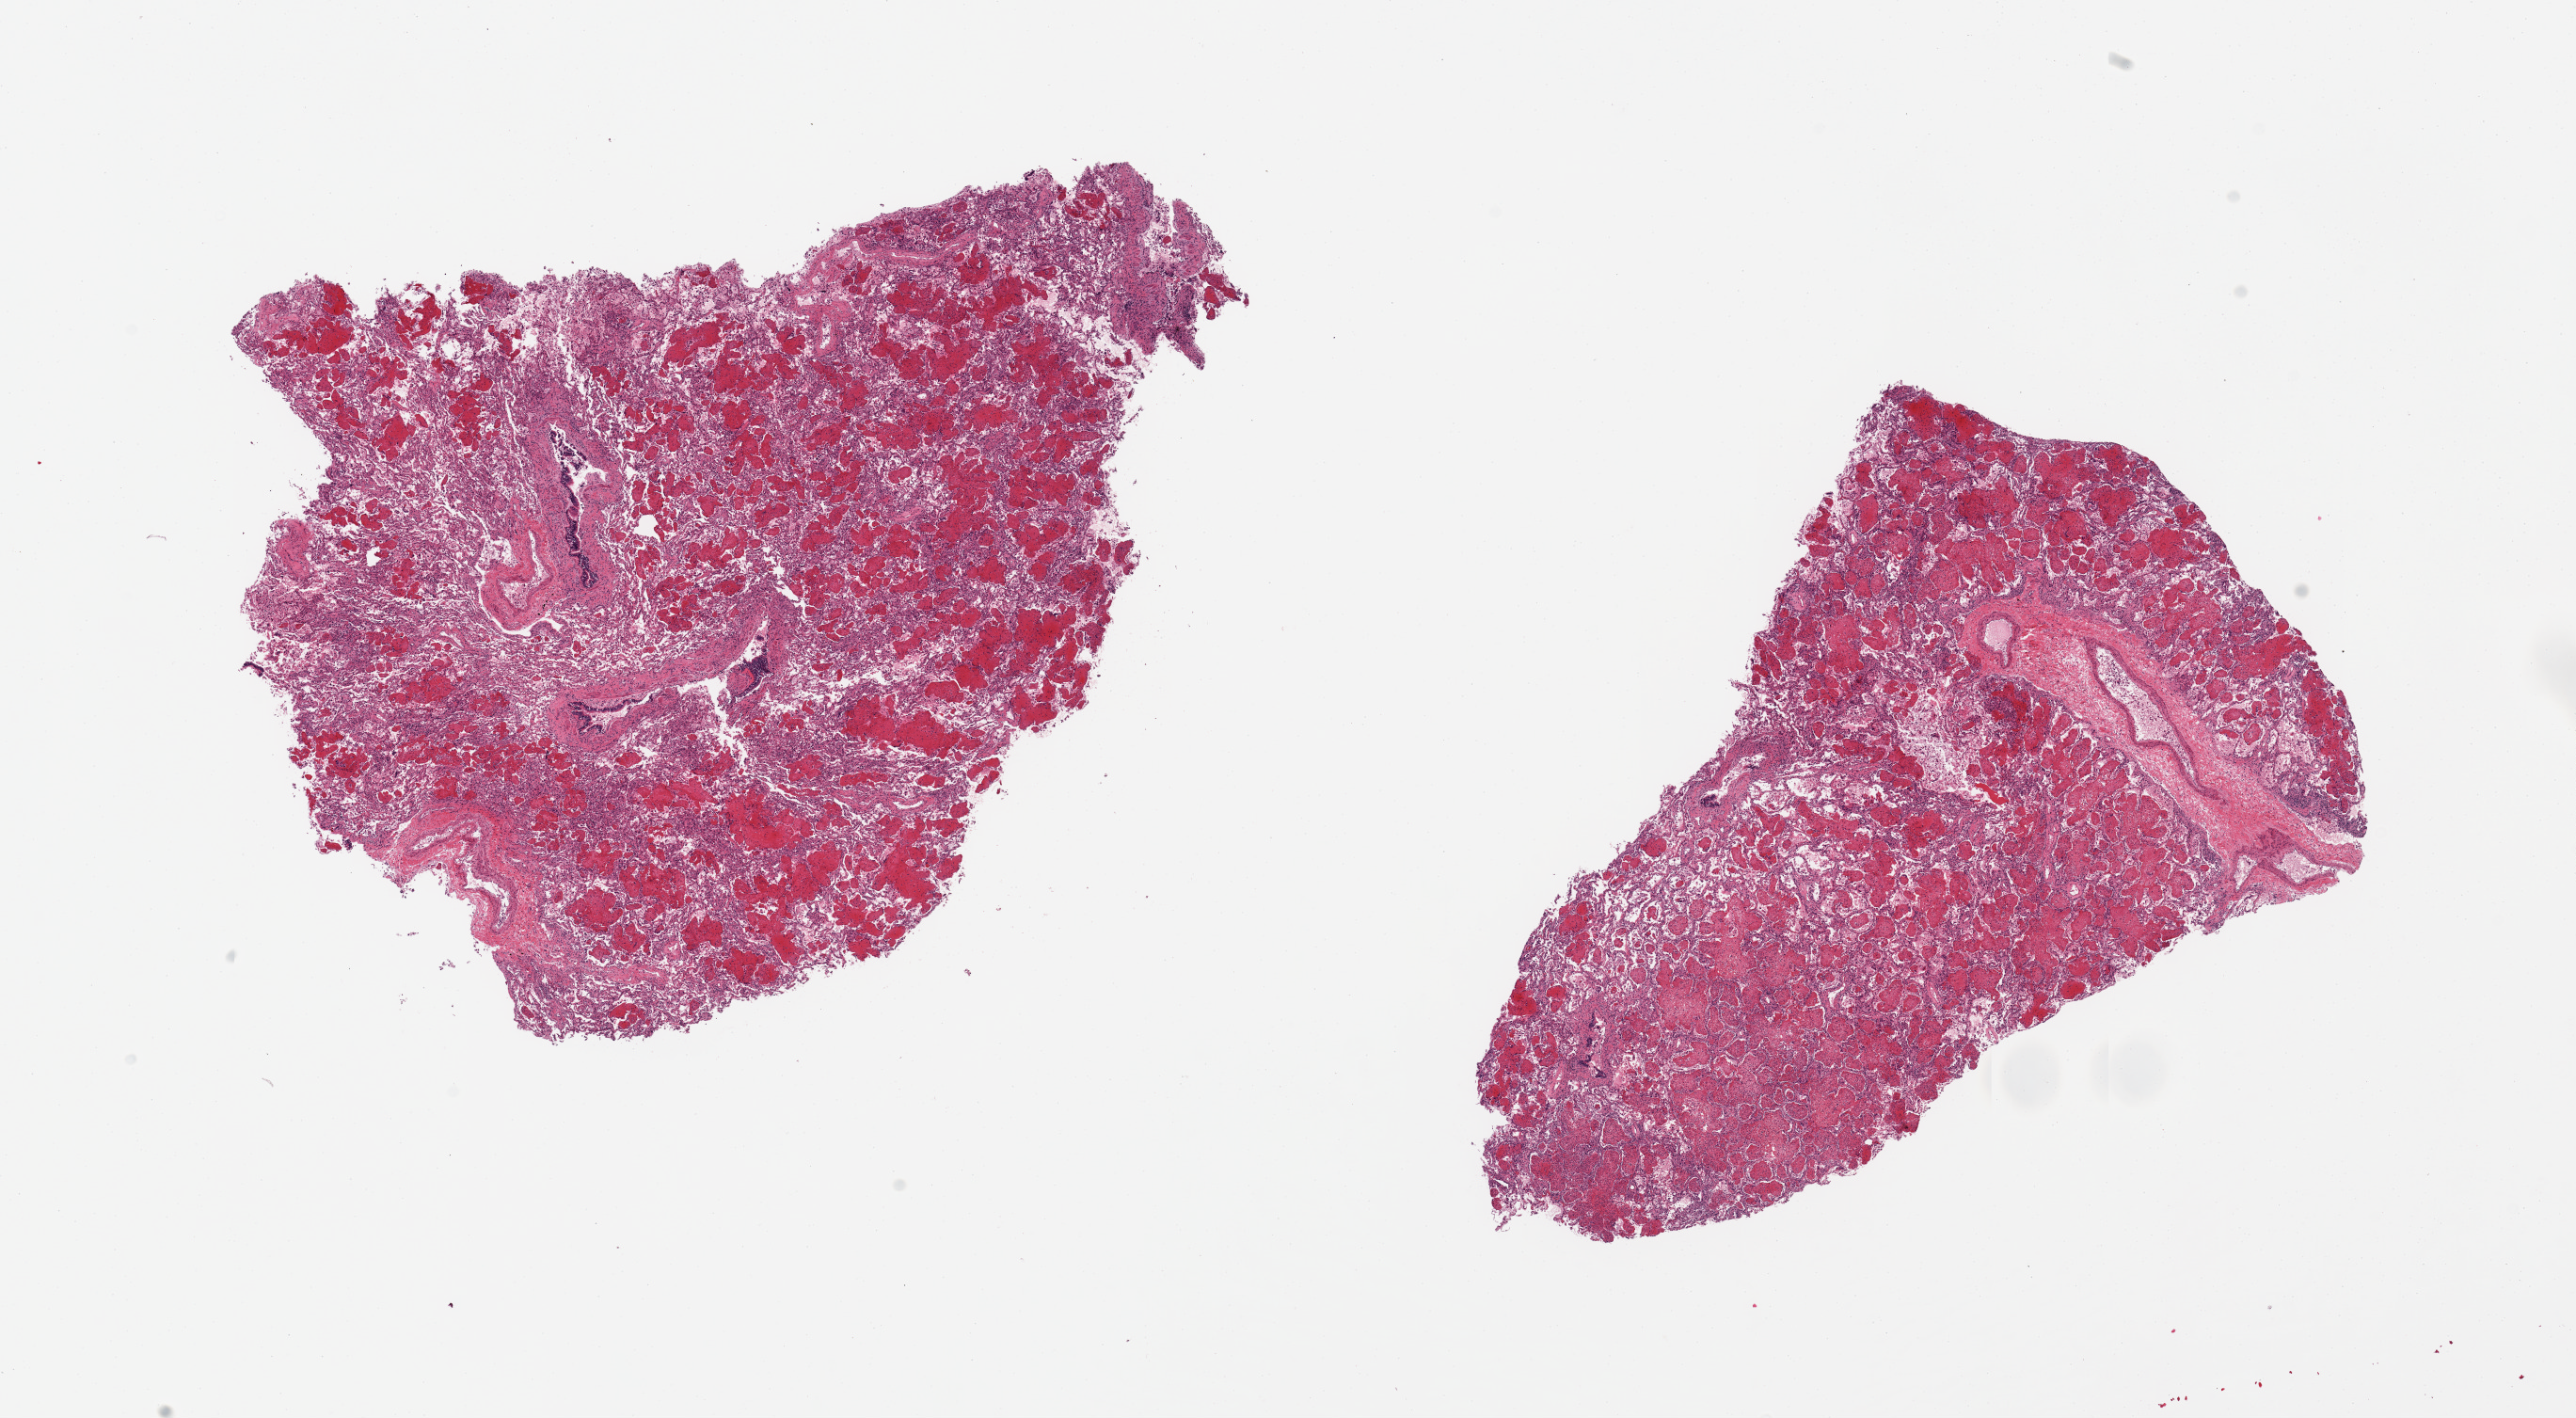
Whole-slide image, haematoxylin and eosin stain, shown as a low-resolution overview of the whole scanned area (about 21.7 x 11.9 mm, acquisition: 20x scan). PAXgene-fixed, paraffin-embedded tissue. Target tissue: lung. Tissue donor sample. Donor sex: female.
- reviewer comment on this tissue sample: 2 pieces; extensive hemorrhage/clot